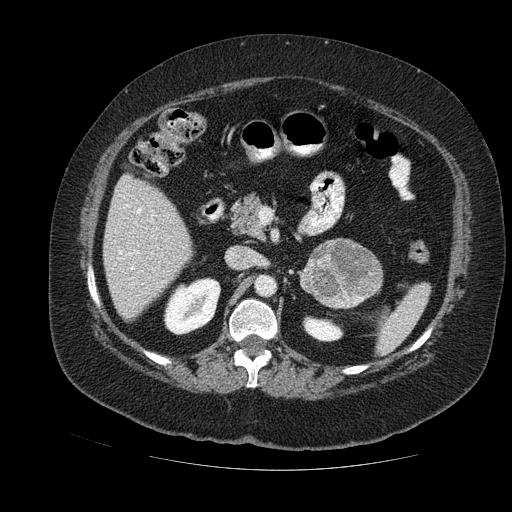
Contrast-enhanced abdominal CT, one axial slice. Position 66 of 121 along the scan axis. Soft-tissue window (W 400 / L 40 HU). 2.5 mm slice thickness. 512 × 512 image matrix, field of view 420 × 420 mm. Female patient. Case-level facts recorded for this patient, not image findings: diagnosis: adrenocortical carcinoma; tumour side: left adrenal; tumour size at pathology: 8 cm; Ki-67 index: 7 %; stage (as recorded): 2.
Outlined on this slice (semi-automatically segmented with operator editing):
- mass: bounding box <301,240,380,305> (left, top, right, bottom; pixels)